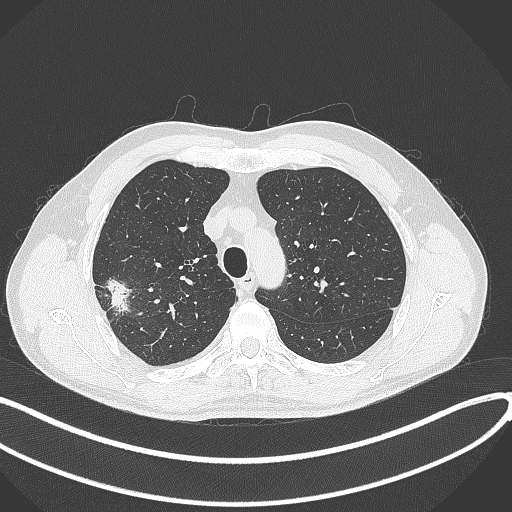
Chest CT, one axial slice; slice 319 of 381 in the series (ordered by position); lung window (W 1500 / L -600 HU); 1 mm slice thickness; 512 × 512 image matrix, field of view 400 × 400 mm. Male patient, age 62 years. From the clinical record (not read from this slice): clinical TNM (as recorded): T1c N0 M0.
Outlined on this slice (rectangle marked by the reading radiologist):
- lung tumour (recorded histology: adenocarcinoma): bounding box (x1, y1, x2, y2) in pixels: (105, 274, 133, 315)